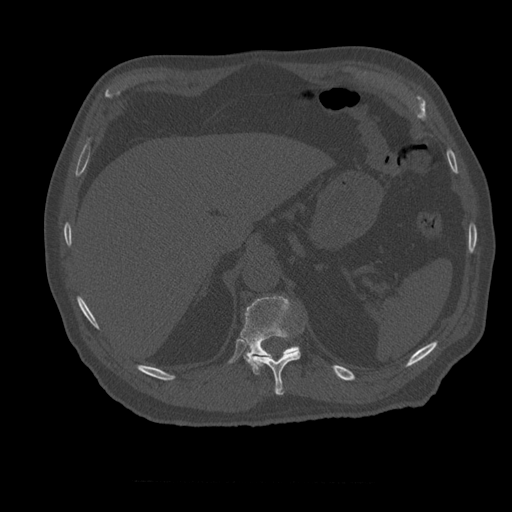
CT including the spine, one axial slice; position 273 of 399 along the scan axis; 120 kVp; bone window (W 1800 / L 400 HU); 1.25 mm slice thickness; 512 × 512 image matrix, field of view 407 × 407 mm. Patient age 73 years. Case-level facts recorded for this patient, not image findings: primary cancer: prostate; vertebrae with lytic lesions (as recorded): L2.
Annotated regions visible in this slice (semi-automatic segmentation, software-assisted and operator-edited):
- T11 vertebra: bounding box (x1, y1, x2, y2) in pixels: (248, 351, 301, 396)
- T12 vertebra: (240, 296, 300, 364)